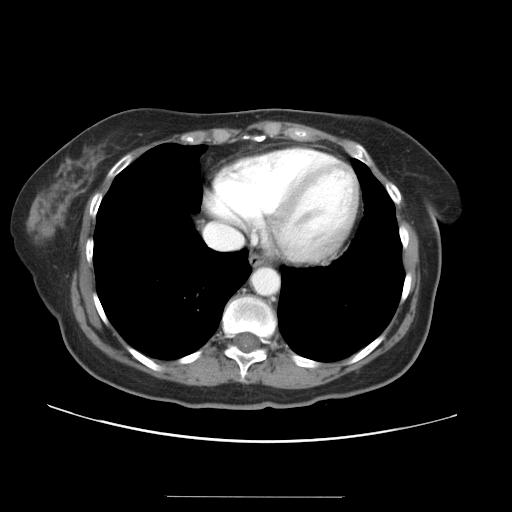
Contrast-enhanced abdominal CT, one axial slice; slice 33 of 34 in the series (ordered by position); soft-tissue window (W 400 / L 40 HU); 512 × 512 image matrix. Female patient, age 69 years. From the clinical record (not read from this slice): diagnosis: colorectal cancer liver metastases, imaged before liver resection; multiple liver metastases: yes.
Outlined on this slice (expert manual segmentation):
- hepatic veins: bounding box [x1, y1, x2, y2] px = [205, 150, 335, 249]